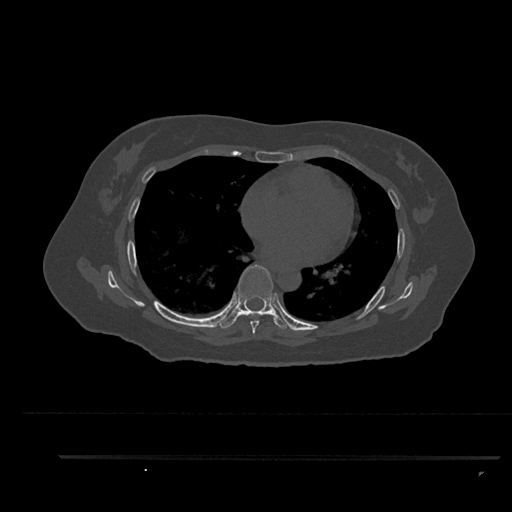
CT including the spine, one axial slice. Position 527 of 797 along the scan axis. 120 kVp. Bone window (W 1800 / L 400 HU). 0.5 mm slice thickness. 512 × 512 image matrix, field of view 408 × 408 mm. Patient: female, 44 years. From the clinical record (not read from this slice): primary cancer: renal; vertebrae with lytic lesions (as recorded): L1.
Outlined on this slice (semi-automatically segmented with operator editing):
- T6 vertebra: bounding box [x1, y1, x2, y2] px = [250, 314, 260, 334]
- T7 vertebra: [216, 264, 290, 329]